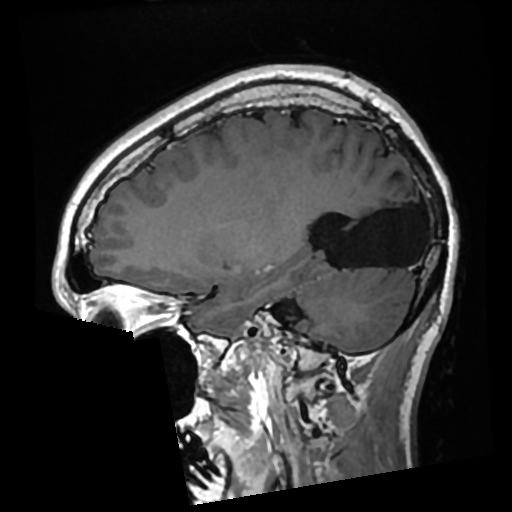
Brain MRI from a brain-tumour surgery series, one sagittal slice. Slice 103 of 276 in the series (ordered by position). T1-weighted post-contrast. 0.7 mm slice thickness. 512 × 512 image matrix, field of view 250 × 250 mm. Case-level facts recorded for this patient, not image findings: histopathology: Glioma with ependymal features; WHO grade: 2; tumour location: Left Parietal.
Outlined on this slice (outlined manually by an expert reader):
- previous resection cavity: box from (x=327, y=184) to (x=424, y=268) px